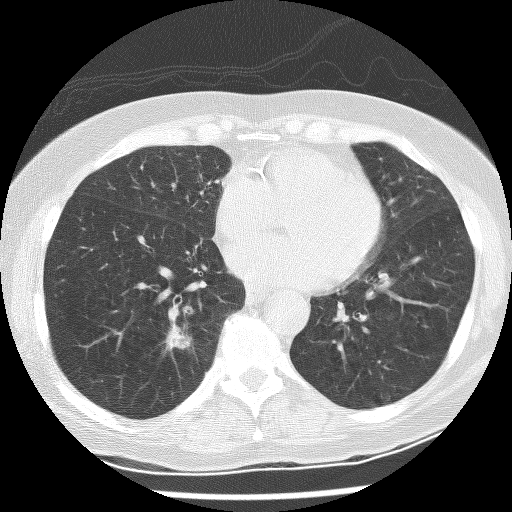
Low-dose screening chest CT, one axial slice. Slice 100 of 247 in the series (ordered by position). 120 kVp. Lung window (W 1500 / L -600 HU). 2.5 mm slice thickness. 512 × 512 image matrix, field of view 300 × 300 mm.
Structures marked on this image (expert manual segmentation):
- lesion 1 (tumor, lower lobe of right lung): bounding box (x1, y1, x2, y2) in pixels: (165, 323, 192, 352)